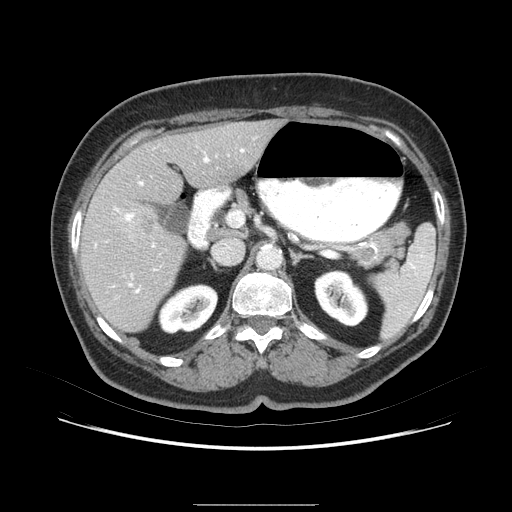
Contrast-enhanced abdominal CT (liver protocol), one axial slice; slice 41 of 79 in the series (ordered by position); 120 kVp; soft-tissue window (W 400 / L 40 HU); 512 × 512 image matrix, field of view 380 × 380 mm. Case-level facts recorded for this patient, not image findings: diagnosis: hepatocellular carcinoma (patient treated with transarterial chemoembolisation; whether this scan precedes or follows treatment is not stated here); TNM stage (as recorded): Stage-I; Child-Pugh class: A; tumour nodularity: uninodular.
Structures marked on this image (semi-automatic segmentation, software-assisted and operator-edited):
- liver parenchyma outside the tumour (the mass and vessels are separate outlines, so this box may not span the whole liver): box from (x=80, y=122) to (x=288, y=340) px
- mass: (x=124, y=201)–(x=170, y=249)
- liver vessels: (x=120, y=147)–(x=259, y=311)